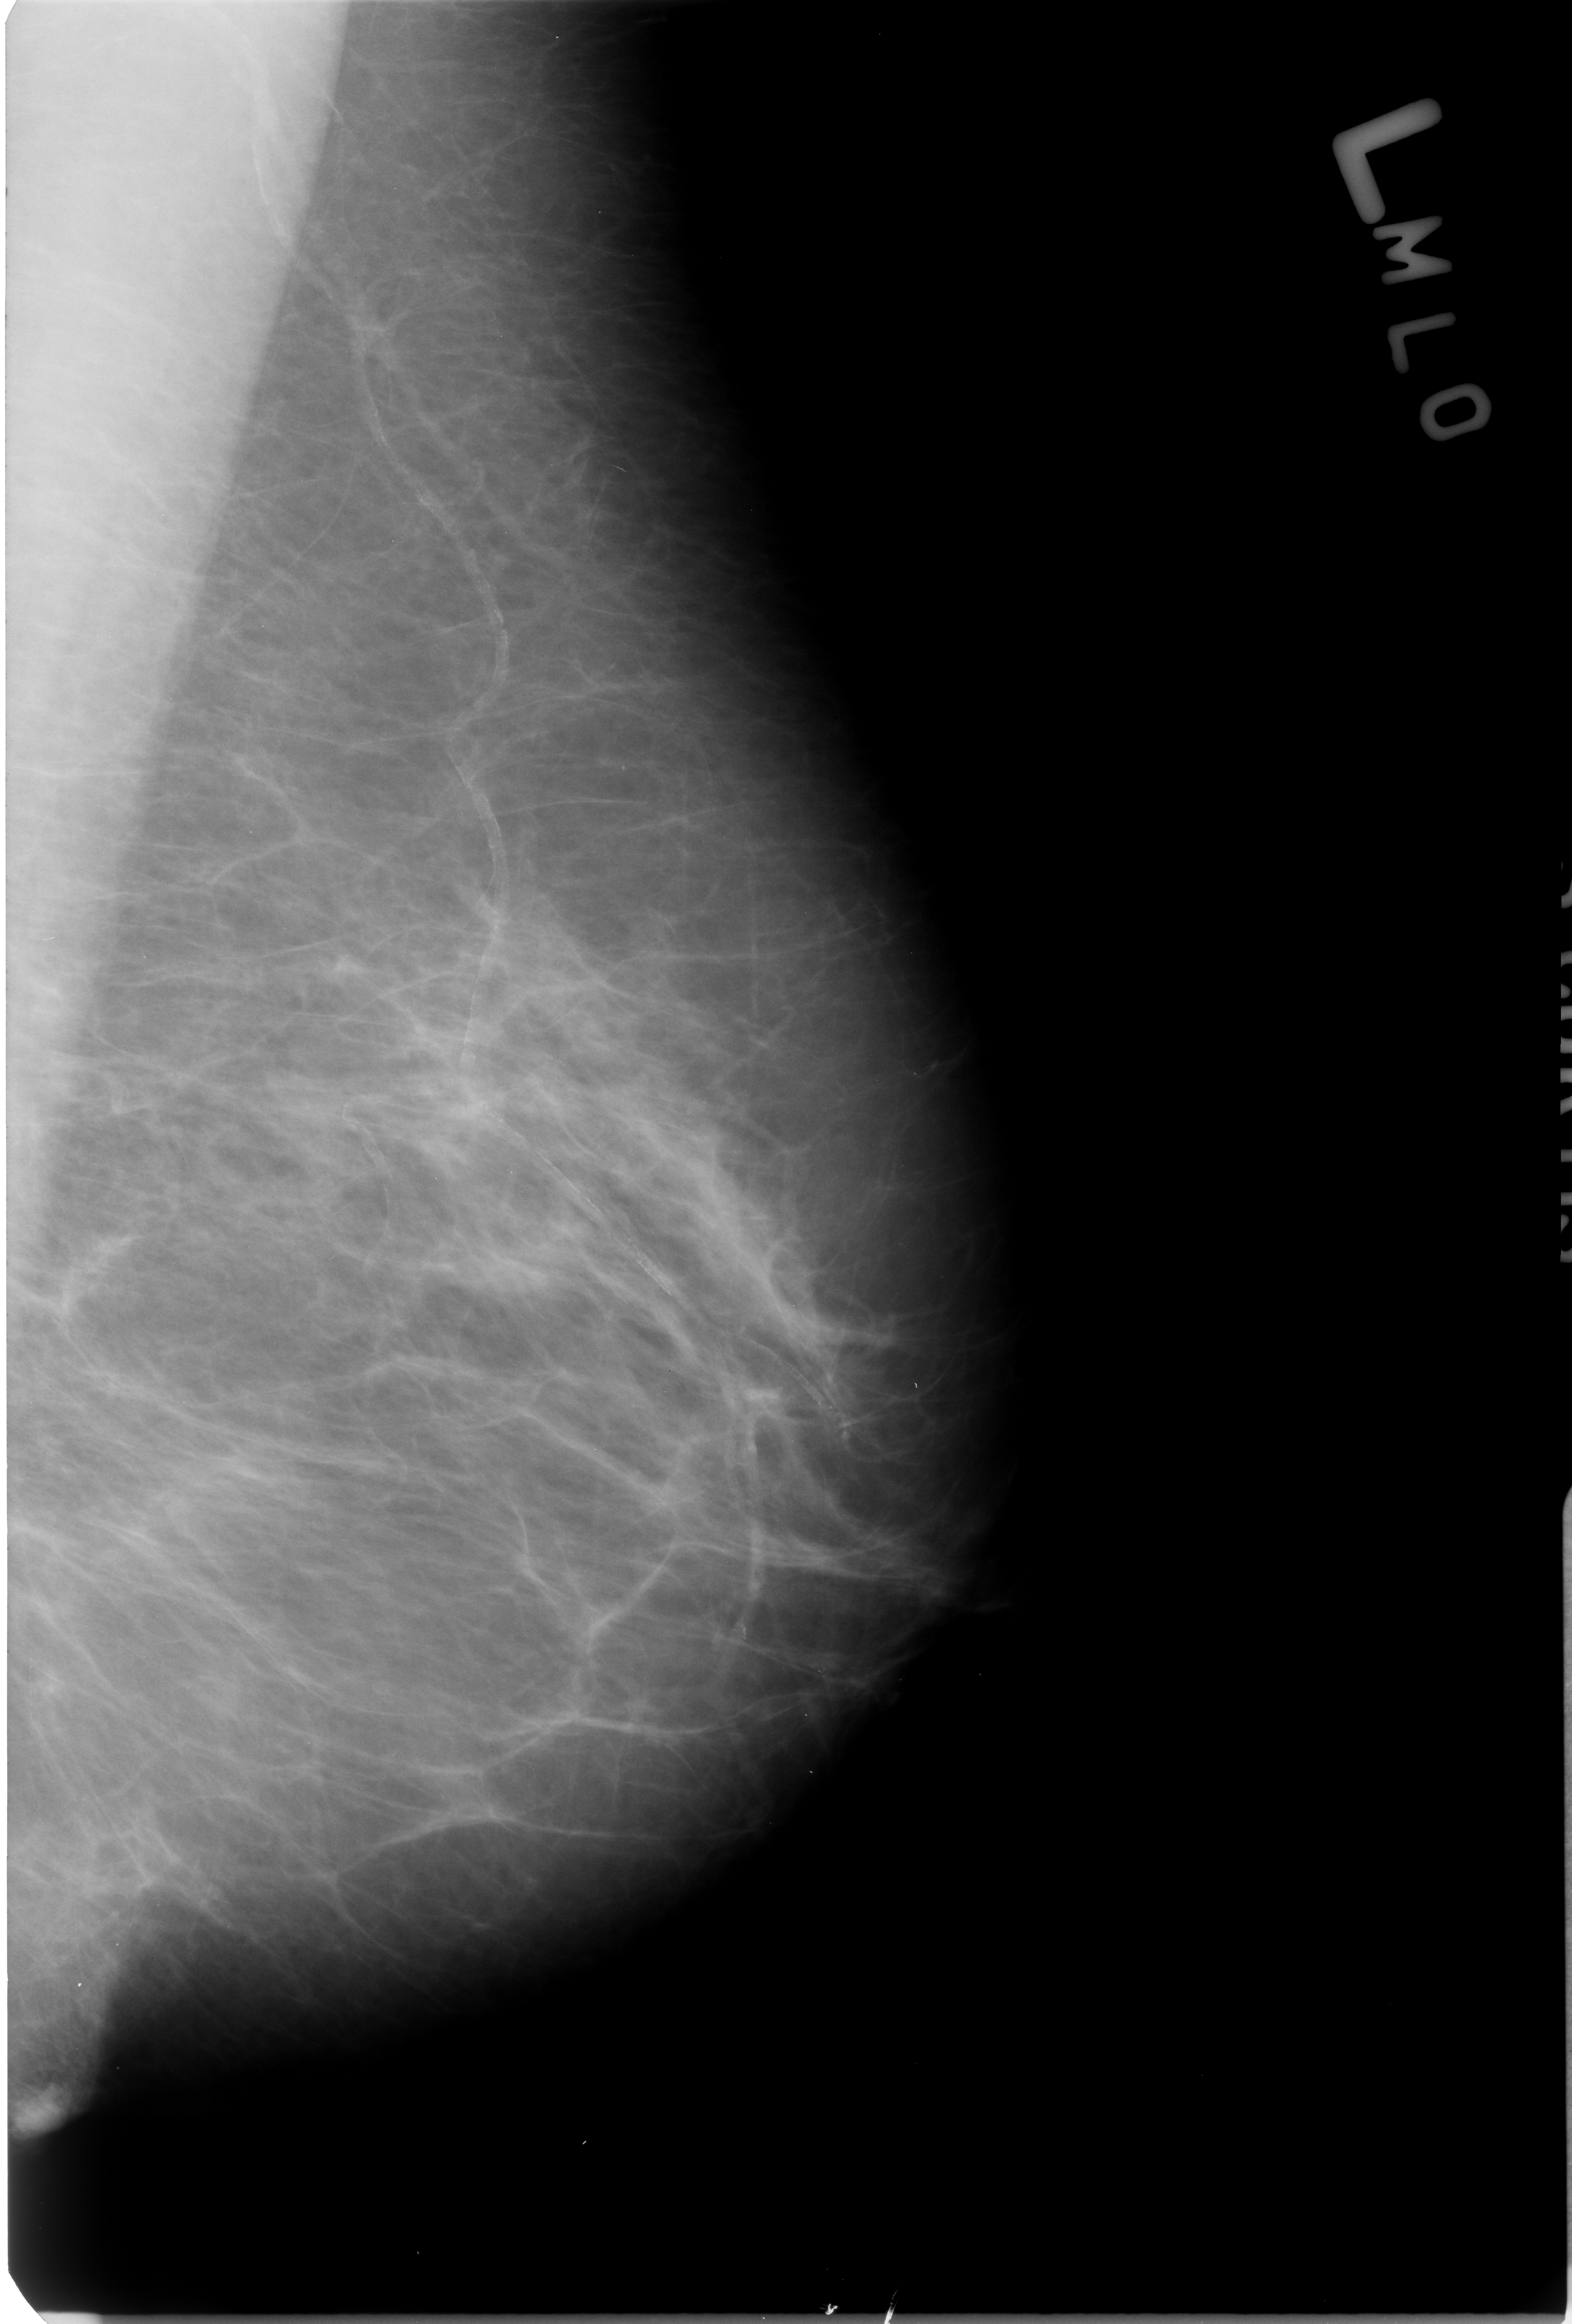
Digitized screen-film mammogram, left breast, mediolateral oblique (MLO) view, breast composition: scattered fibroglandular densities (BI-RADS density category 2 of 4).
- Marked findings (only marked abnormalities are described; nothing is implied about the rest of the image): Finding 1 of 2: calcifications, morphology vascular; BI-RADS assessment category 2; subtlety rating 3 on a 1 (subtle) to 5 (obvious) scale; benign; no additional work-up was recommended (benign without callback).
- Finding 2 of 2: calcifications, morphology vascular; BI-RADS assessment category 2; subtlety rating 3 on a 1 (subtle) to 5 (obvious) scale; benign; no additional work-up was recommended (benign without callback).